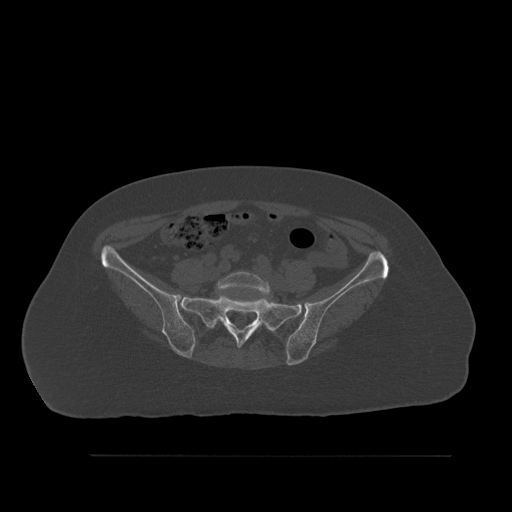
CT including the spine, one axial slice; slice 177 of 527 in the series (ordered by position); bone window (W 1800 / L 400 HU); 1.5 mm slice thickness; 512 × 512 image matrix. Patient: female, 73 years. From the clinical record (not read from this slice): primary cancer: breast; vertebrae with lytic lesions (as recorded): L2.
Annotated regions visible in this slice (semi-automatic segmentation, software-assisted and operator-edited):
- L5 vertebra: bounding box <216,271,272,329> (left, top, right, bottom; pixels)